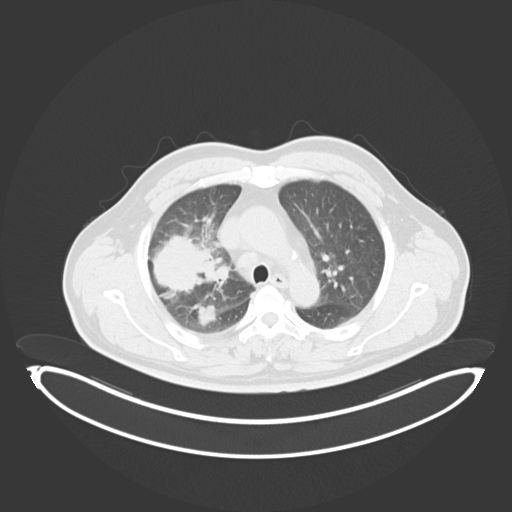
Chest CT, one axial slice. Slice 221 of 284 in the series (ordered by position). Reconstruction kernel B30f. 120 kVp. Lung window (W 1500 / L -600 HU). 512 × 512 image matrix, field of view 500 × 500 mm. Patient: male, 55 years. Case-level facts recorded for this patient, not image findings: clinical TNM (as recorded): T3 N2 M1.
Structures marked on this image (rectangle marked by the reading radiologist):
- lung tumour (recorded histology: adenocarcinoma): bounding box (x1, y1, x2, y2) in pixels: (148, 231, 219, 299)